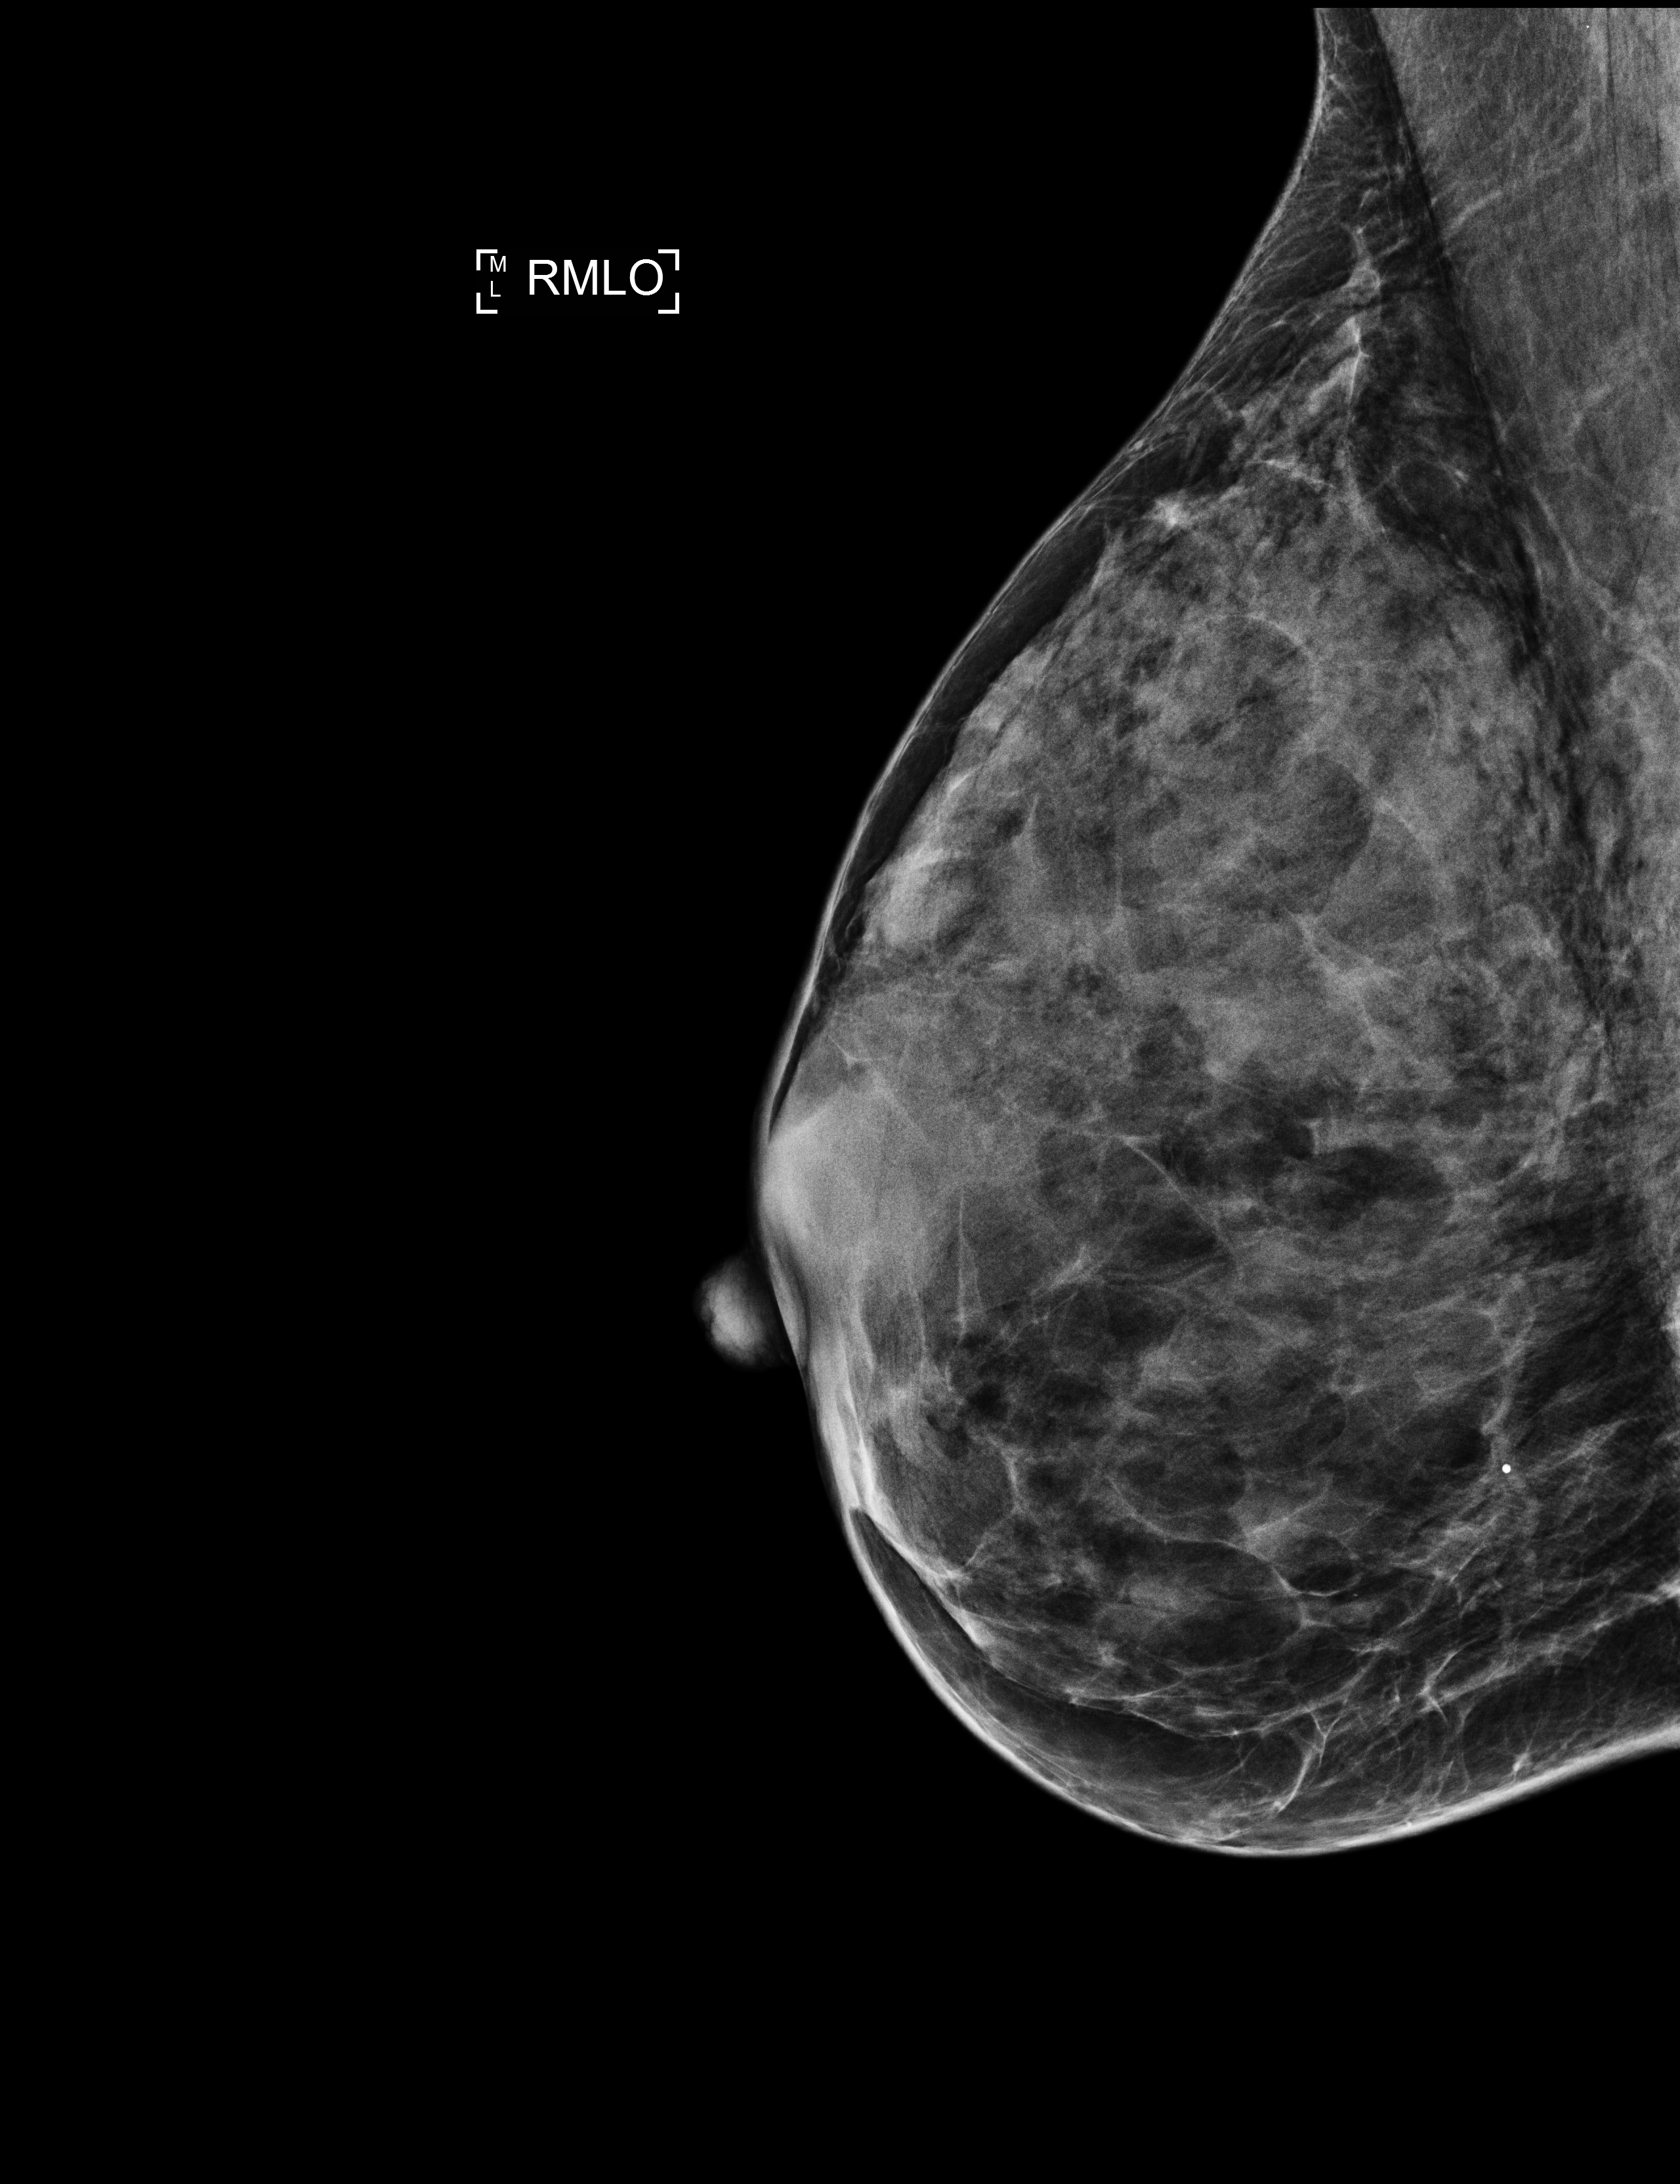
Screening examination. Patient aged 56 years (female).
Image type: full-field digital mammogram. Breast: right. Projection: medio-lateral oblique projection.